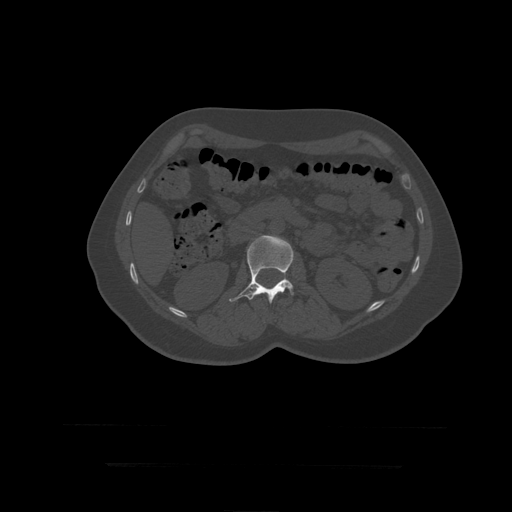
CT including the spine, one axial slice. Position 149 of 399 along the scan axis. Reconstruction kernel STANDARD. Bone window (W 1800 / L 400 HU). 1.25 mm slice thickness. 512 × 512 image matrix, field of view 450 × 450 mm. Patient age 41 years. From the clinical record (not read from this slice): primary cancer: breast.
Structures marked on this image (semi-automatic segmentation, software-assisted and operator-edited):
- L2 vertebra: bounding box (x1, y1, x2, y2) in pixels: (230, 235, 294, 304)